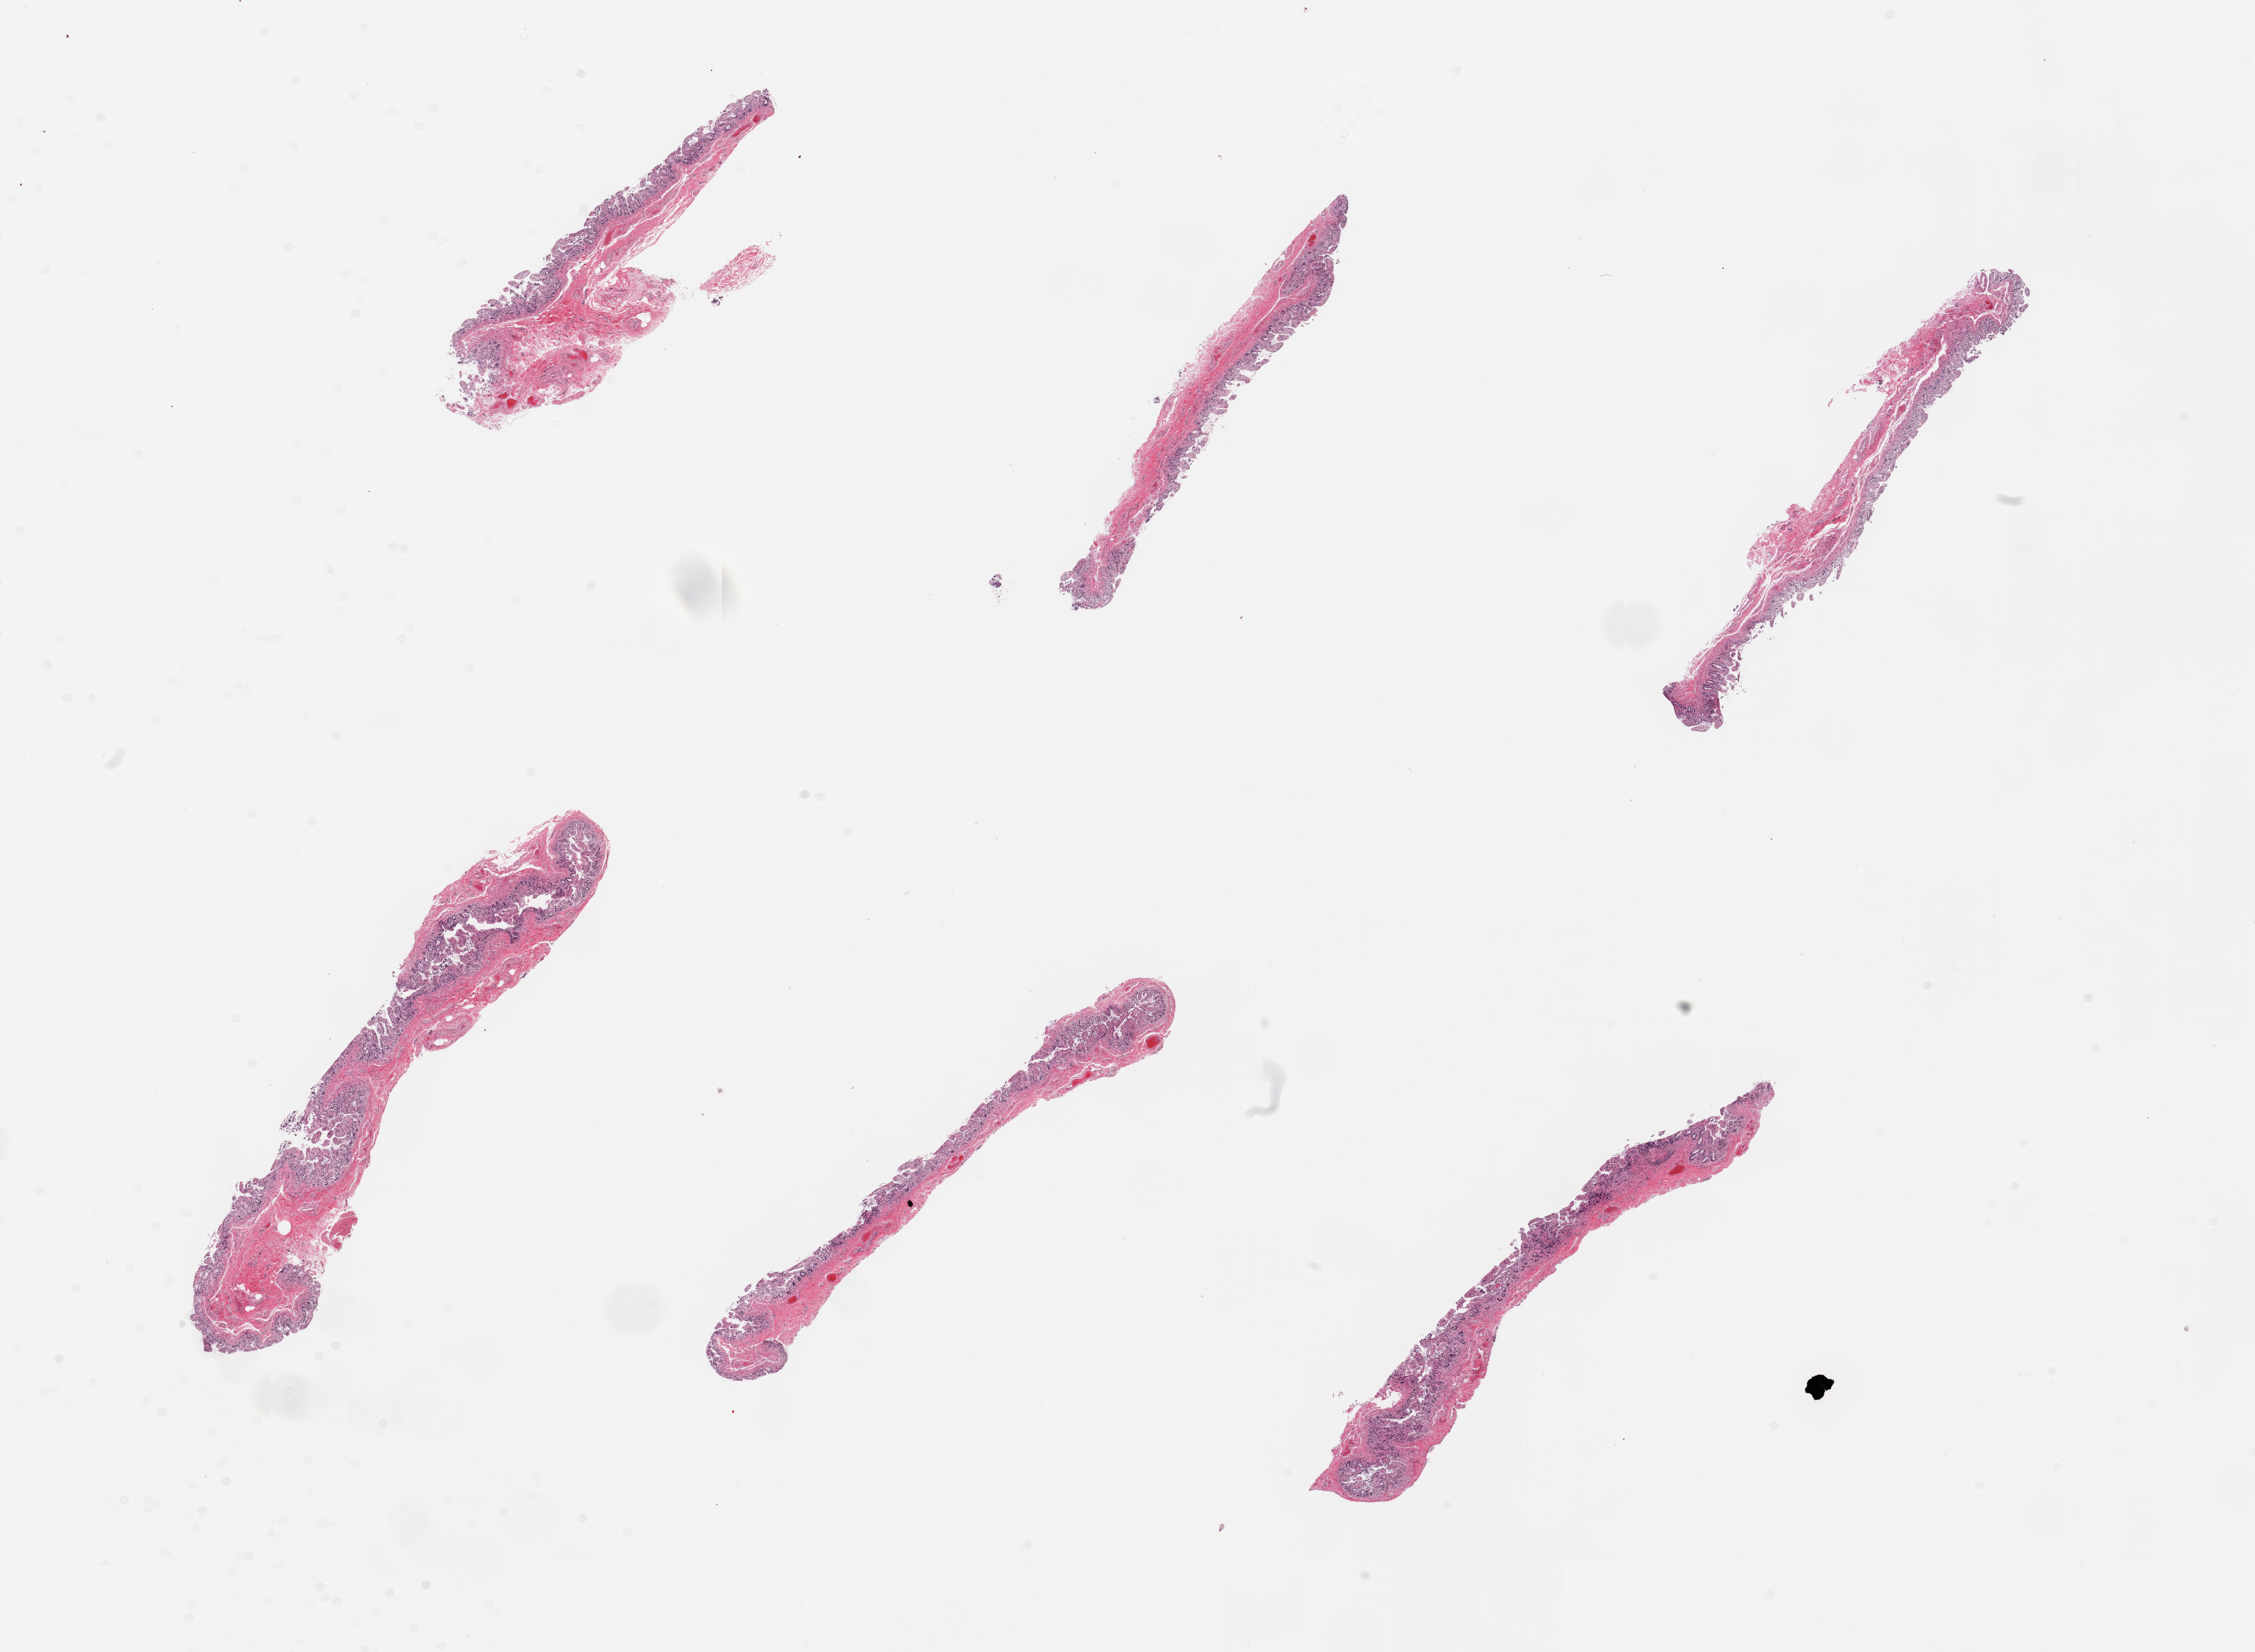
Whole-slide image, hematoxylin and eosin (H&E) stain, brightfield, a low-resolution overview of the entire scanned area, about 24.6 x 18.0 mm, PAXgene-fixed paraffin-embedded (PFPE) section, section of ileum (target tissue), donor tissue sample. Donor sex: male.
Pathologist's review note for this sample: 6 pieces; well sampled autolyzed mucosa, but no lymphoid nodules present.